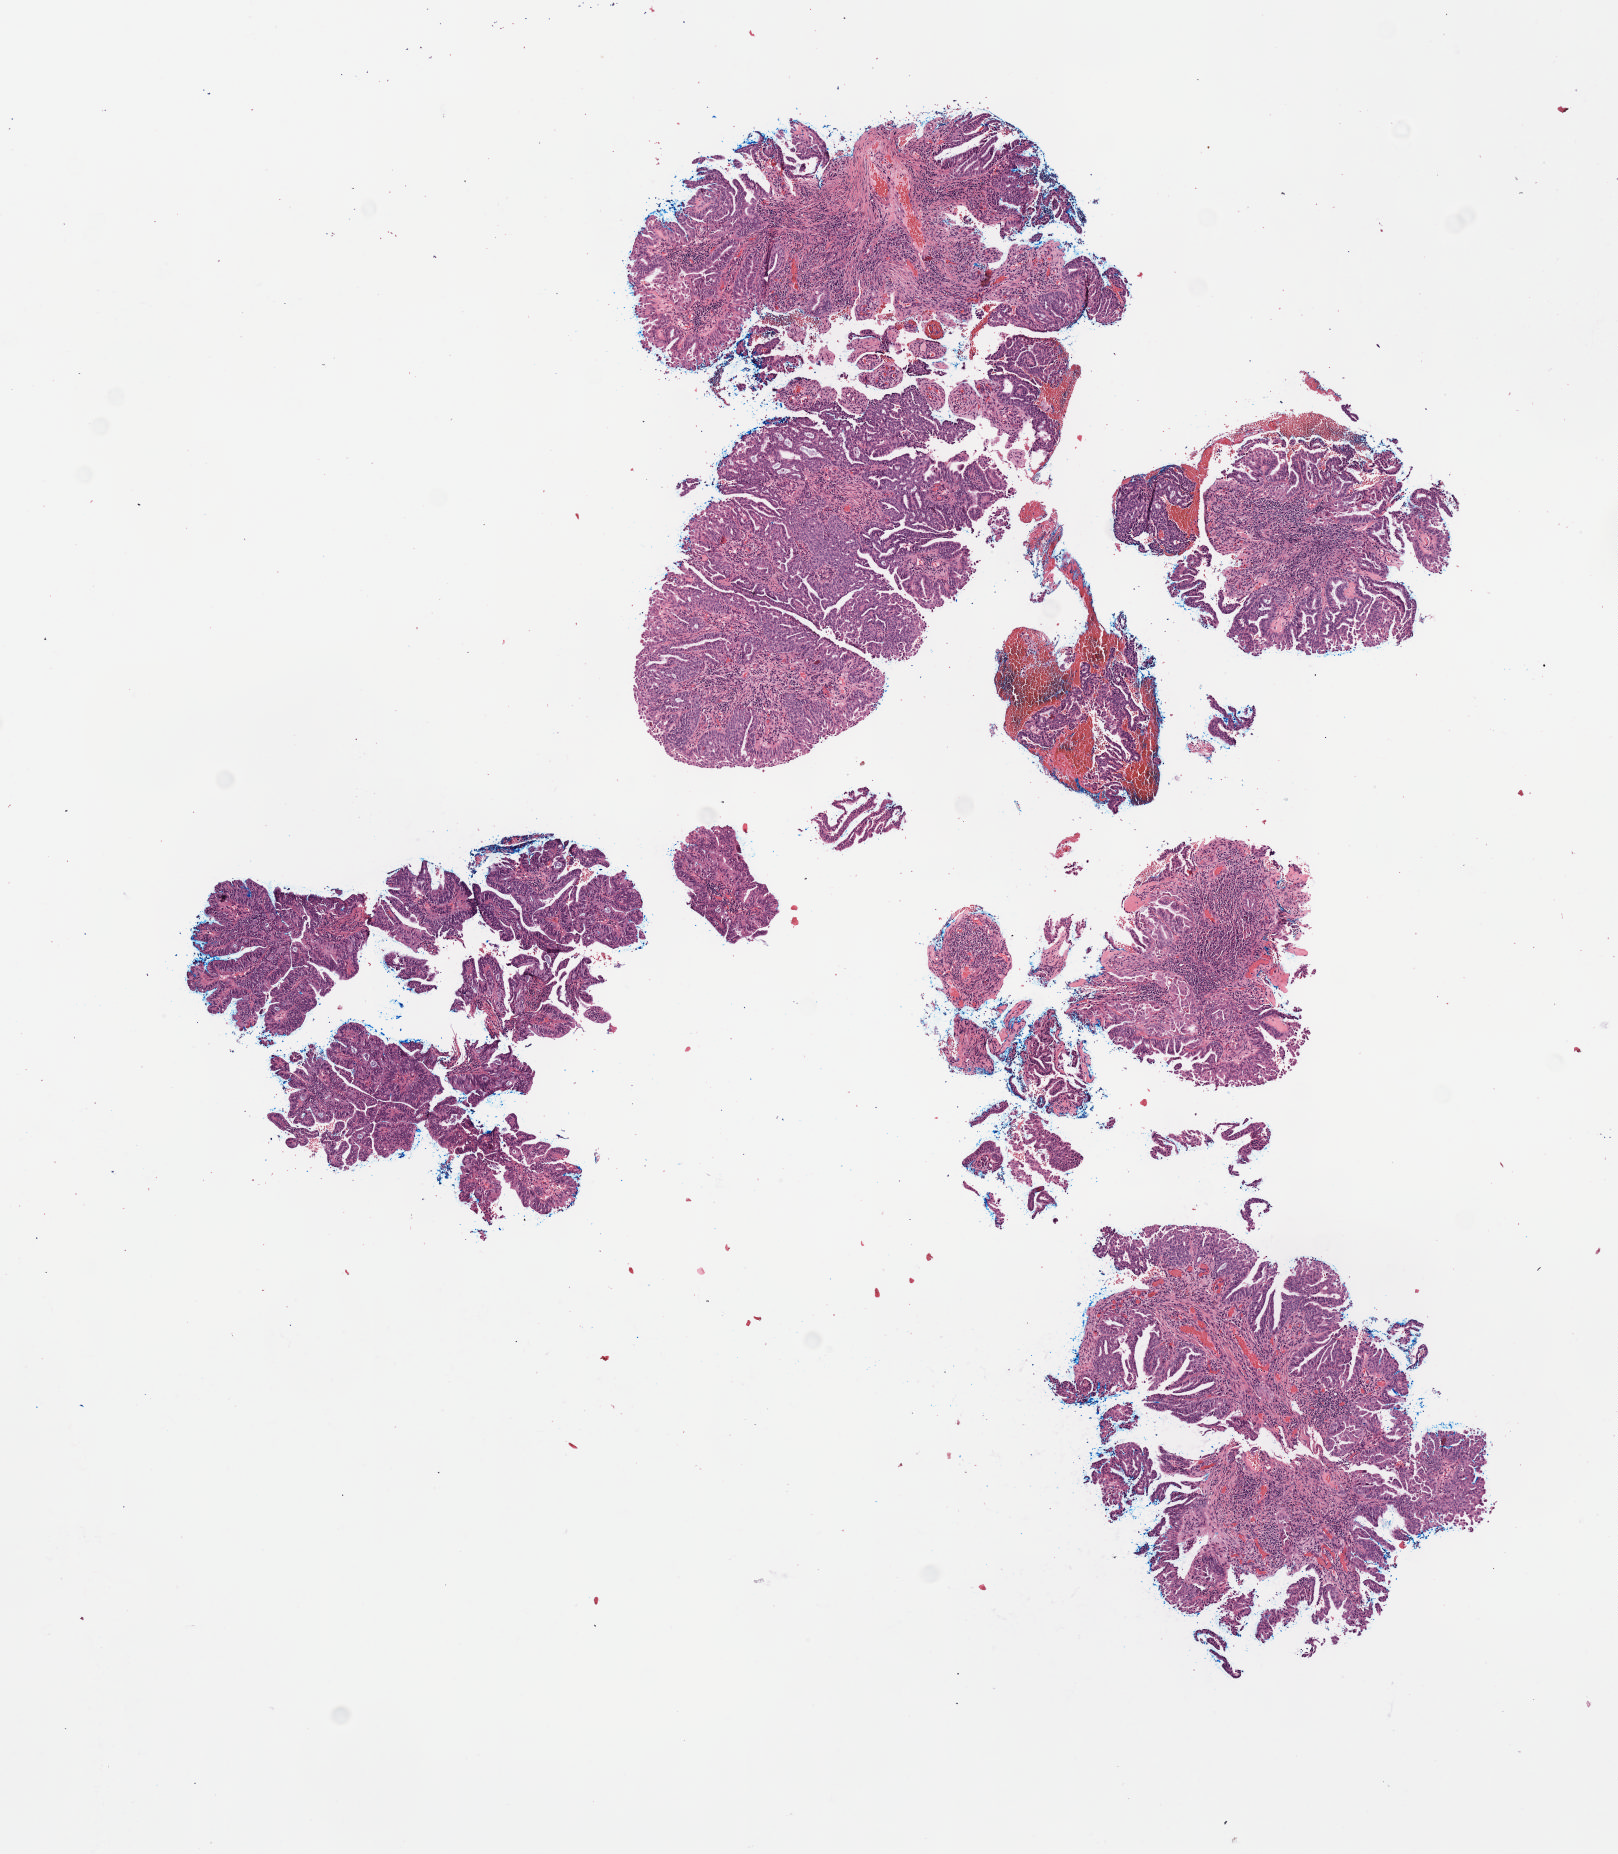
H&E-stained whole-slide image, a low-resolution overview of the entire scanned area, about 6.5 x 7.5 mm (from a 40x scan), formalin-fixed paraffin-embedded (FFPE) diagnostic section, cervix, primary tumour sample. Patient: female, age at initial diagnosis 53 years.
Pathologic diagnosis: Mucinous adenocarcinoma, endocervical type (cervix uteri).